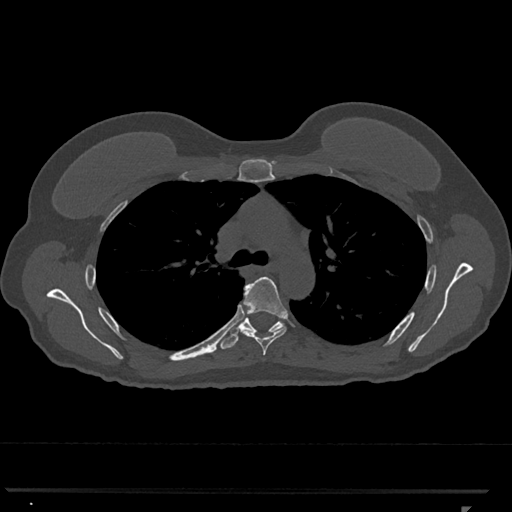
CT including the spine, one axial slice. Position 790 of 793 along the scan axis. Reconstruction kernel Br40s/3. 120 kVp. Bone window (W 1800 / L 400 HU). 512 × 512 image matrix. Patient: female, 62 years. From the clinical record (not read from this slice): primary cancer: renal.
Structures marked on this image (semi-automatic segmentation, software-assisted and operator-edited):
- T5 vertebra: bounding box <240,277,288,356> (left, top, right, bottom; pixels)
- T6 vertebra: <220,287,283,349>